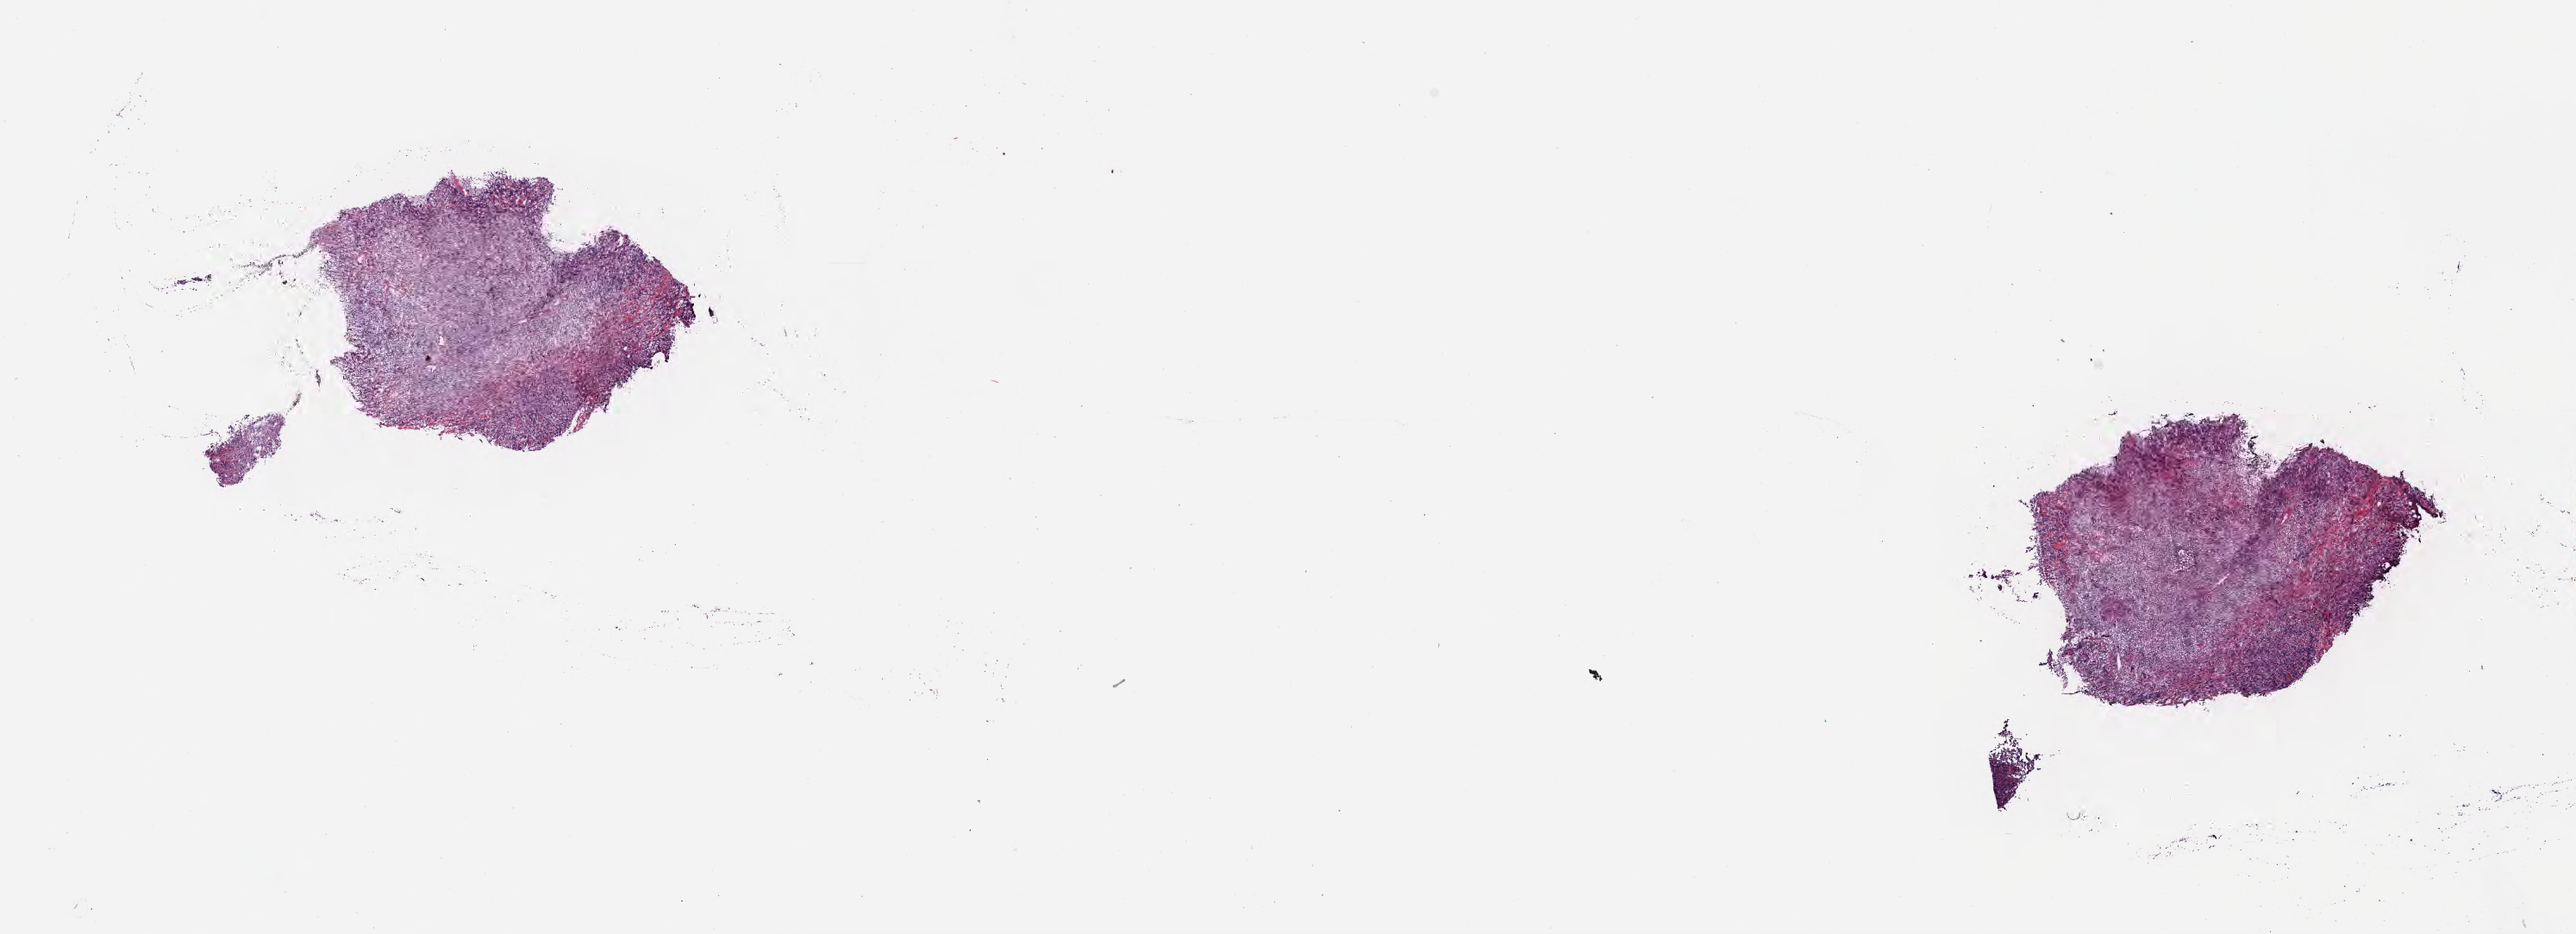
Digitized haematoxylin and eosin-stained section, whole scanned area (about 24.1 x 8.8 mm) shown as a low-resolution overview, frozen section (tissue freezing medium), specimen: primary tumor, site: cranium. Patient: male, 12 years old.
Diagnosis: Diffuse large B-cell lymphoma, NOS.